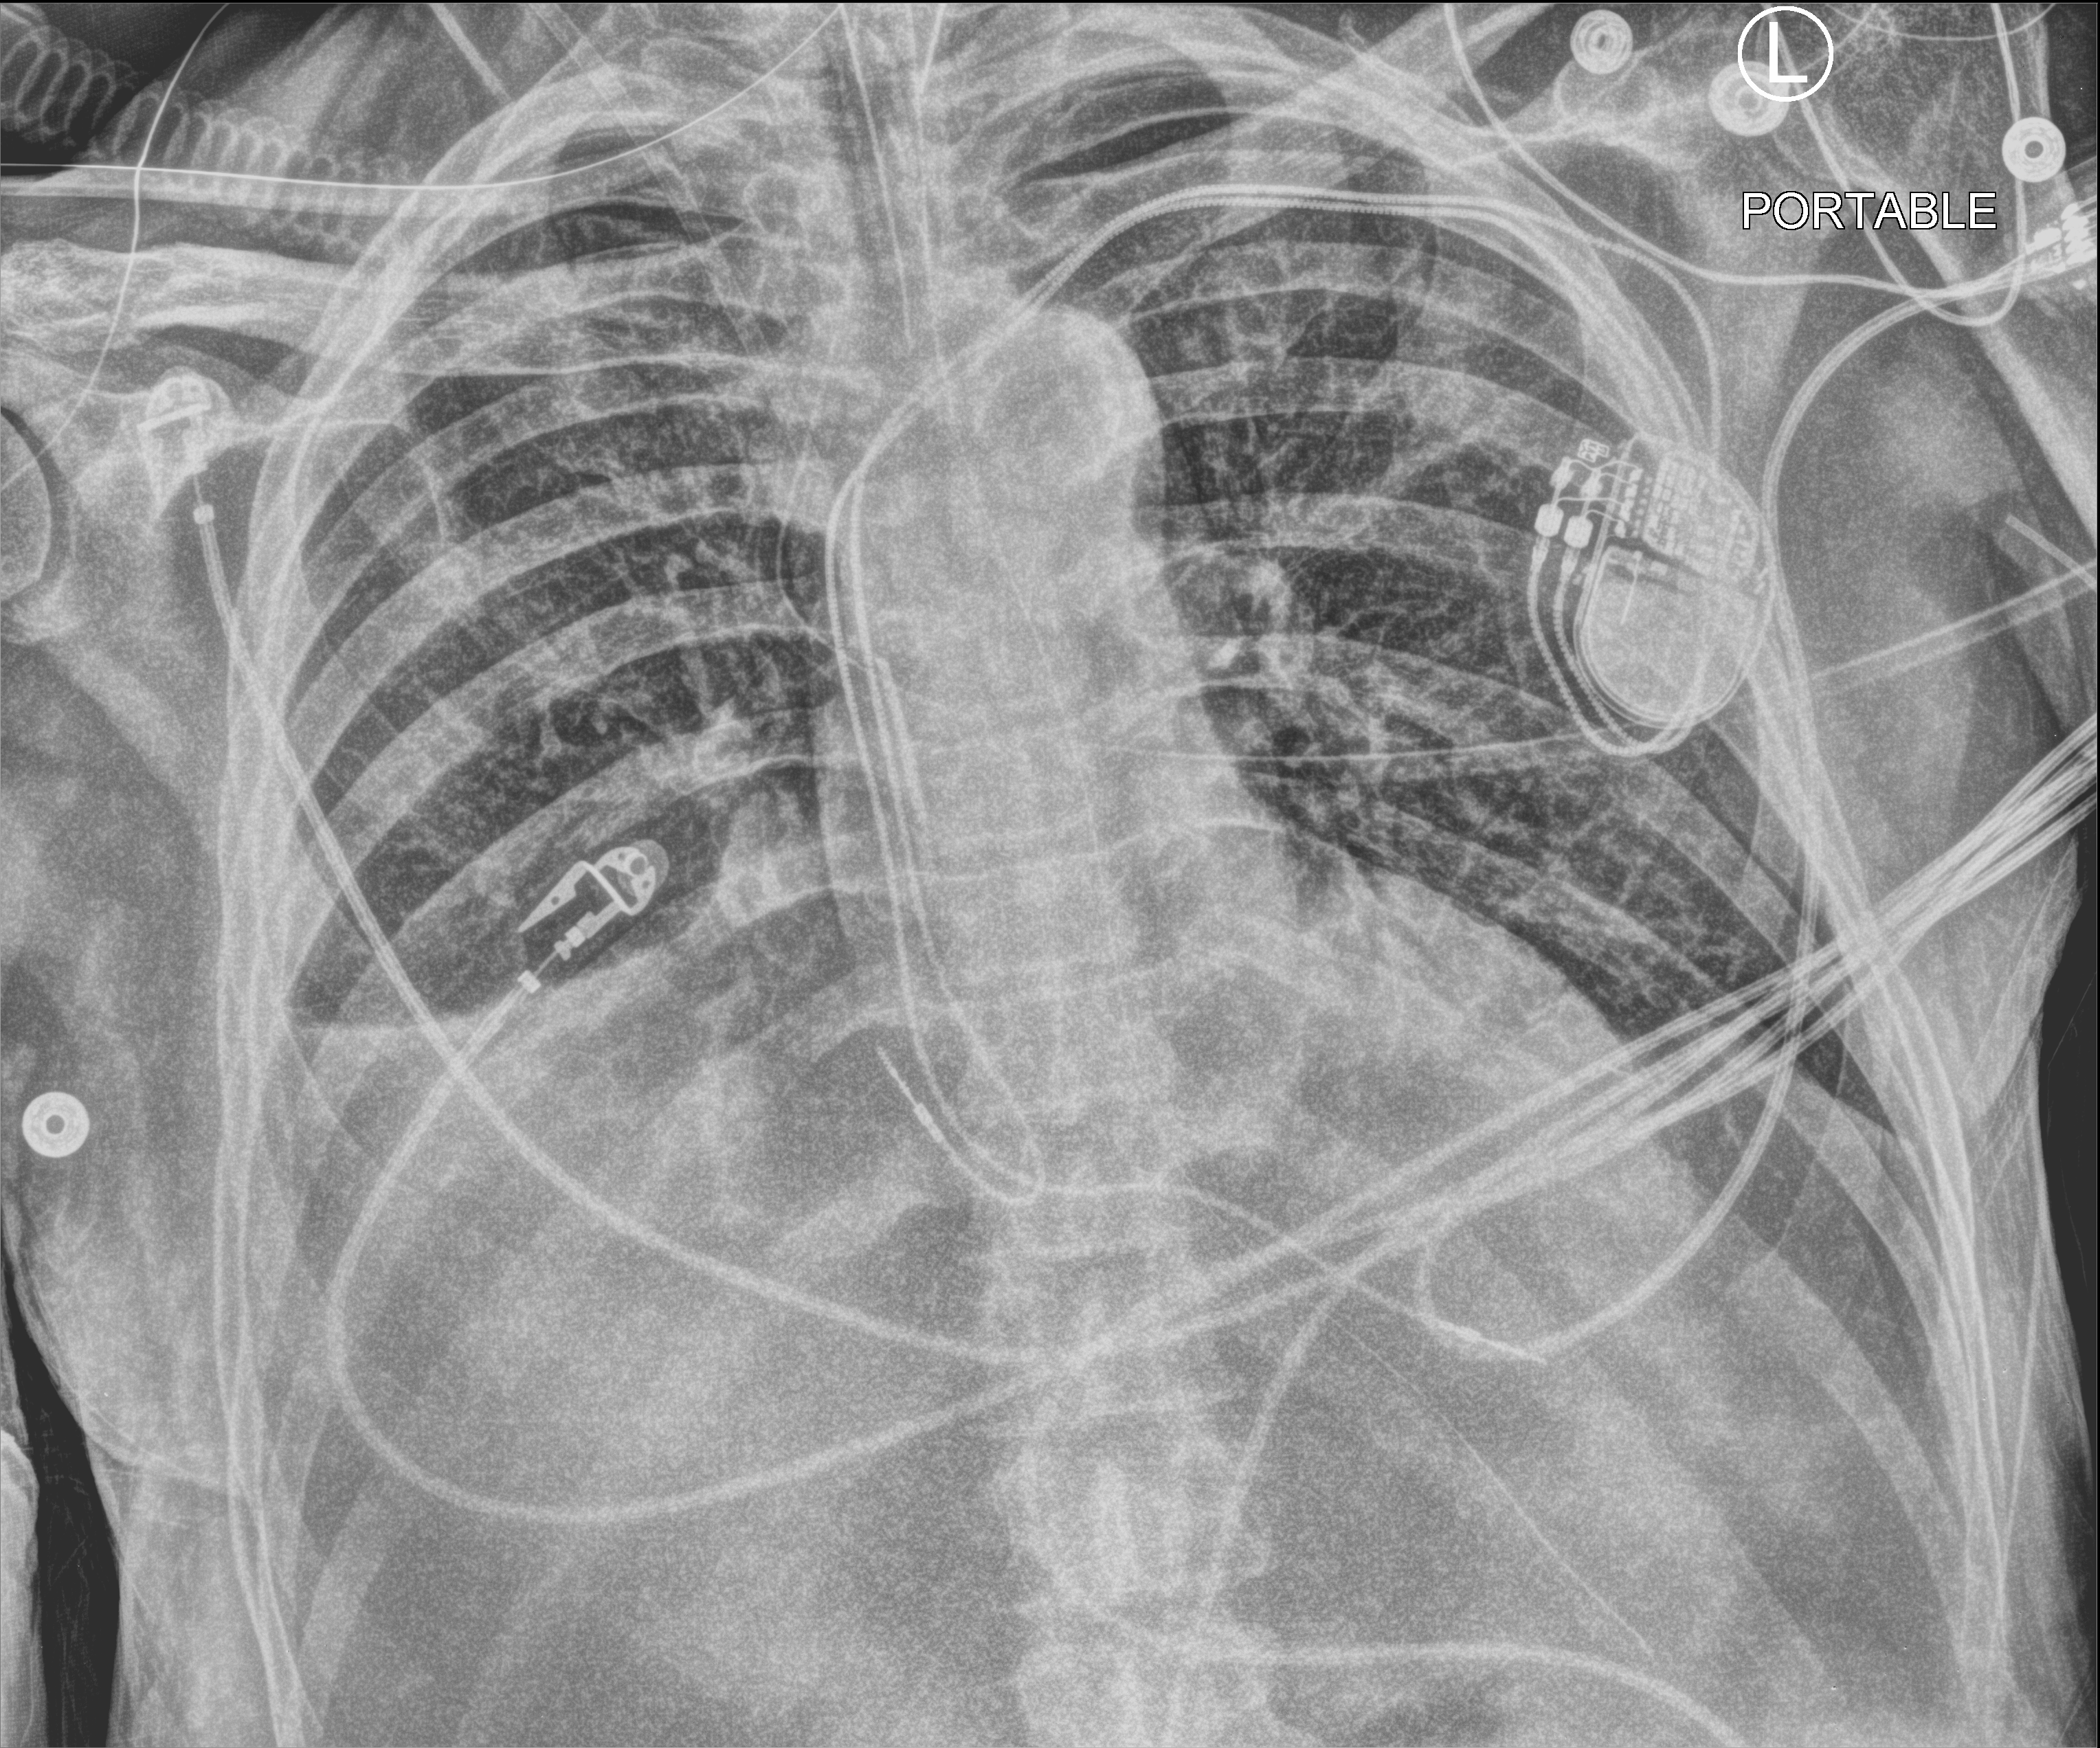
Bedside chest radiograph (computed radiography); anteroposterior (AP) projection. Patient hospitalised with COVID-19; male, aged 60–74 years.
Hospital-stay facts (about this admission, not read from this image; timing relative to this image not recorded): admitted to intensive care during this hospital stay: yes.